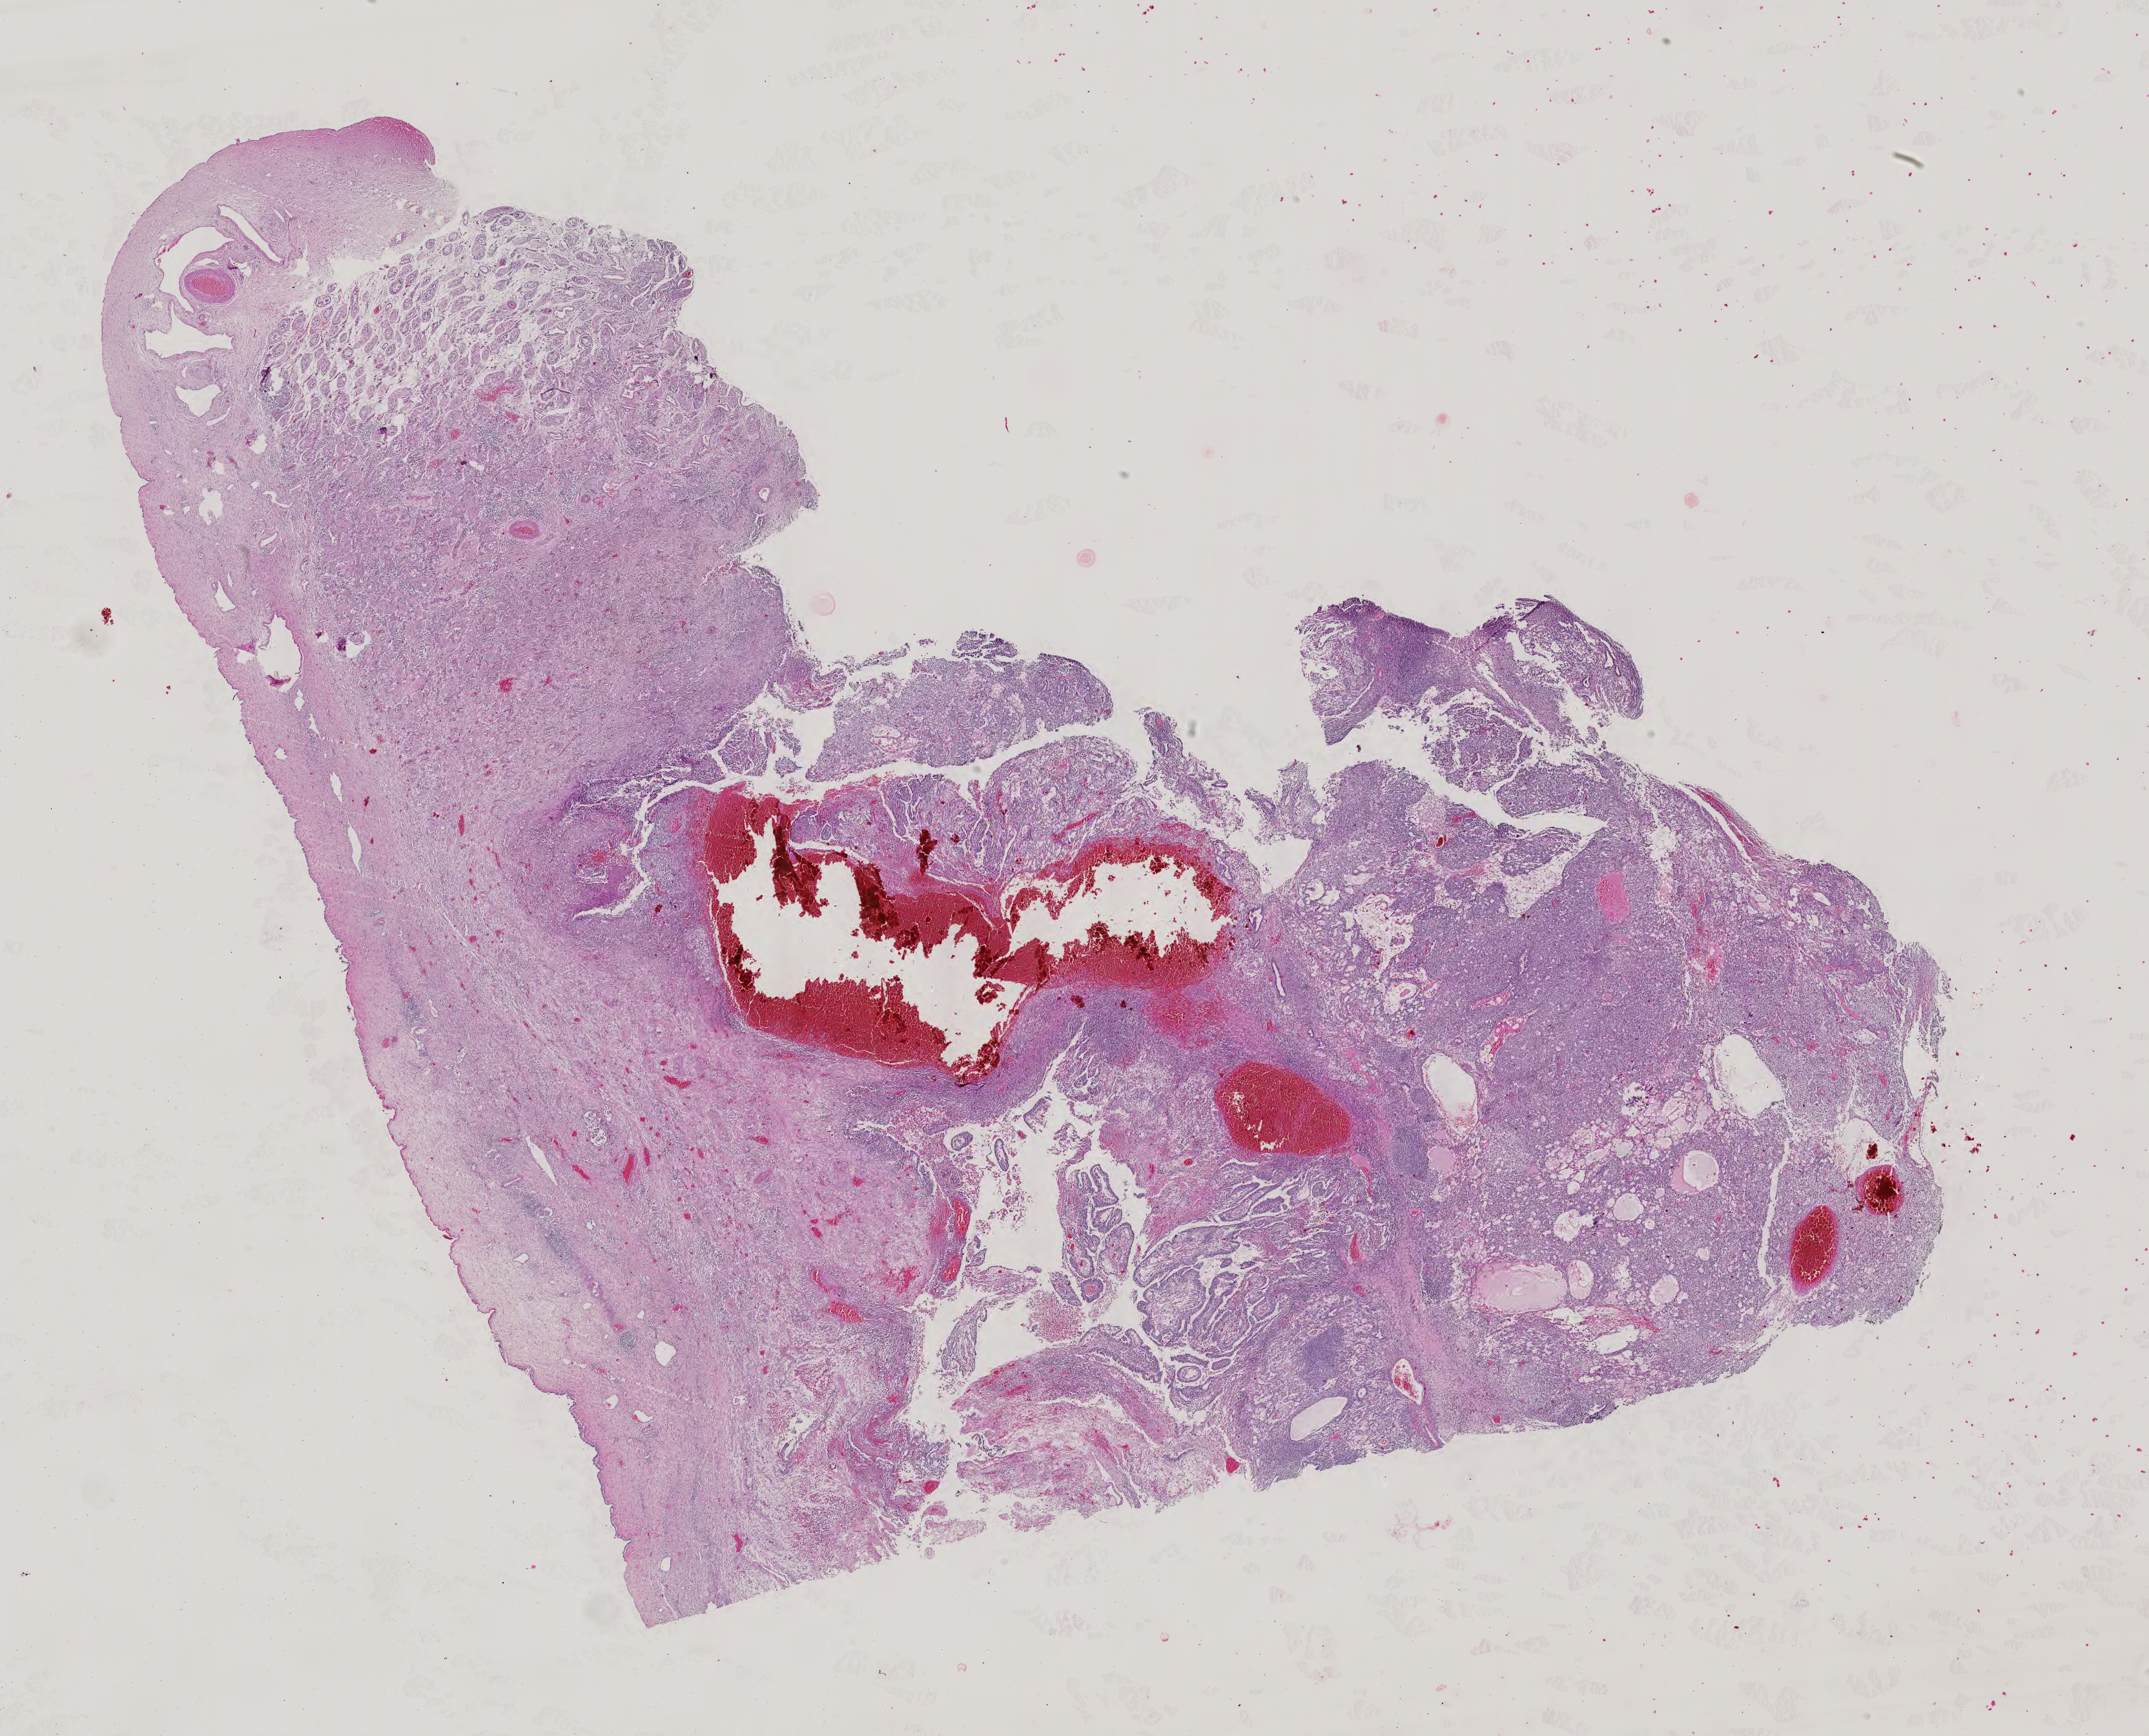
Hematoxylin and eosin (H&E) stained whole-slide image, whole scanned area (about 24.2 x 19.6 mm, slide scanned at 40x) shown as a low-resolution overview. FFPE section. Testis, primary tumour sample. Male patient; age at initial diagnosis 34 years.
• TNM: T1 NX M0
• AJCC pathologic stage: II (4th edition)
• diagnosis: Mixed germ cell tumor